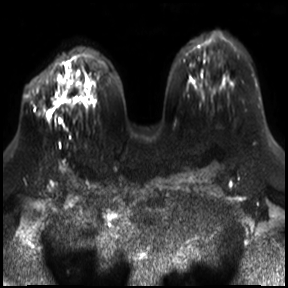
Breast MRI, one axial slice. Slice 19 of 30 in the series (ordered by position). Diffusion-weighted series; image 2 of 4 stored at this slice position (different b-values; order by instance number). 3 T. 4 mm slice thickness. 288 × 288 image matrix. Female patient.
Annotated regions visible in this slice (manually delineated by an expert):
- tumour on diffusion-weighted imaging: box from (x=46, y=85) to (x=66, y=119) px